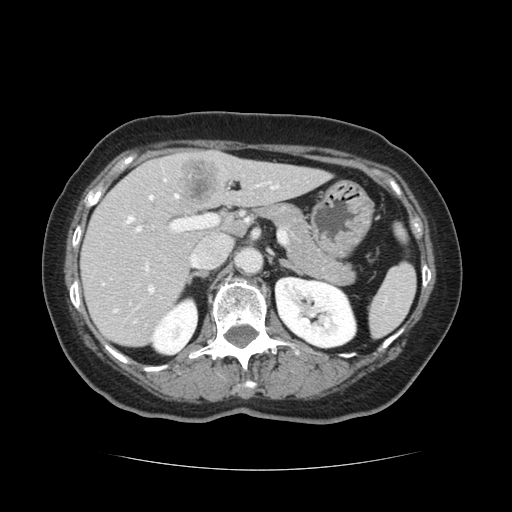
Contrast-enhanced abdominal CT, one axial slice. Position 70 of 128 along the scan axis. 120 kVp. Intravenous contrast given. Soft-tissue window (W 400 / L 40 HU). 2.5 mm slice thickness. 512 × 512 image matrix, field of view 366 × 366 mm. Female patient, age 67 years. Case-level facts recorded for this patient, not image findings: diagnosis: colorectal cancer liver metastases, imaged before liver resection; multiple liver metastases: yes; largest metastasis: 3 cm; chemotherapy before resection: no.
Outlined on this slice (expert manual segmentation):
- hepatic veins: bounding box [x1, y1, x2, y2] px = [115, 186, 278, 312]
- liver: [82, 150, 326, 346]
- planned liver remnant (the part of the liver to remain after resection): [82, 161, 326, 346]
- portal vein (with intrahepatic branches): [135, 181, 272, 294]
- liver metastasis: [176, 159, 220, 207]